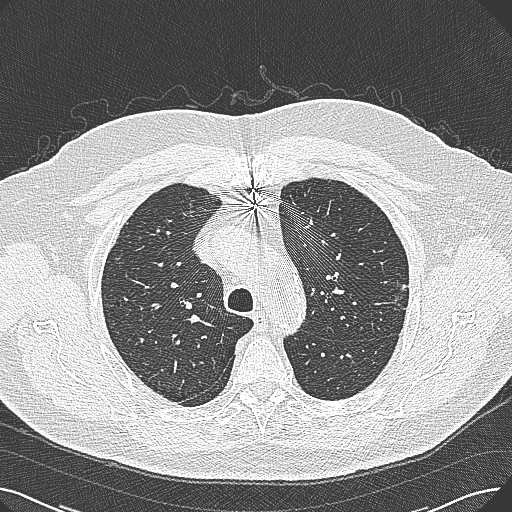
Chest CT (low-dose screening protocol), one axial image; first (baseline) screen; lung window (W 1500 / L -600 HU); slice 71 of 269 in the series. Male, age 74 years at enrolment. Former smoker at enrolment.
Lesion marked by an expert reader, bounding box [x1, y1, x2, y2] px = [377, 272, 422, 315]. Reader record for this screening exam (exam-level; its link to the box is not recorded): non-calcified nodule or mass ≥4 mm, left upper lobe, 15 × 10 mm, poorly defined margins, soft tissue attenuation. Later outcome: lung cancer diagnosed 124 days after this screen — adenocarcinoma, NOS, left upper lobe, well differentiated (G1), stage IA (AJCC 6th edition), 26 mm at pathology.